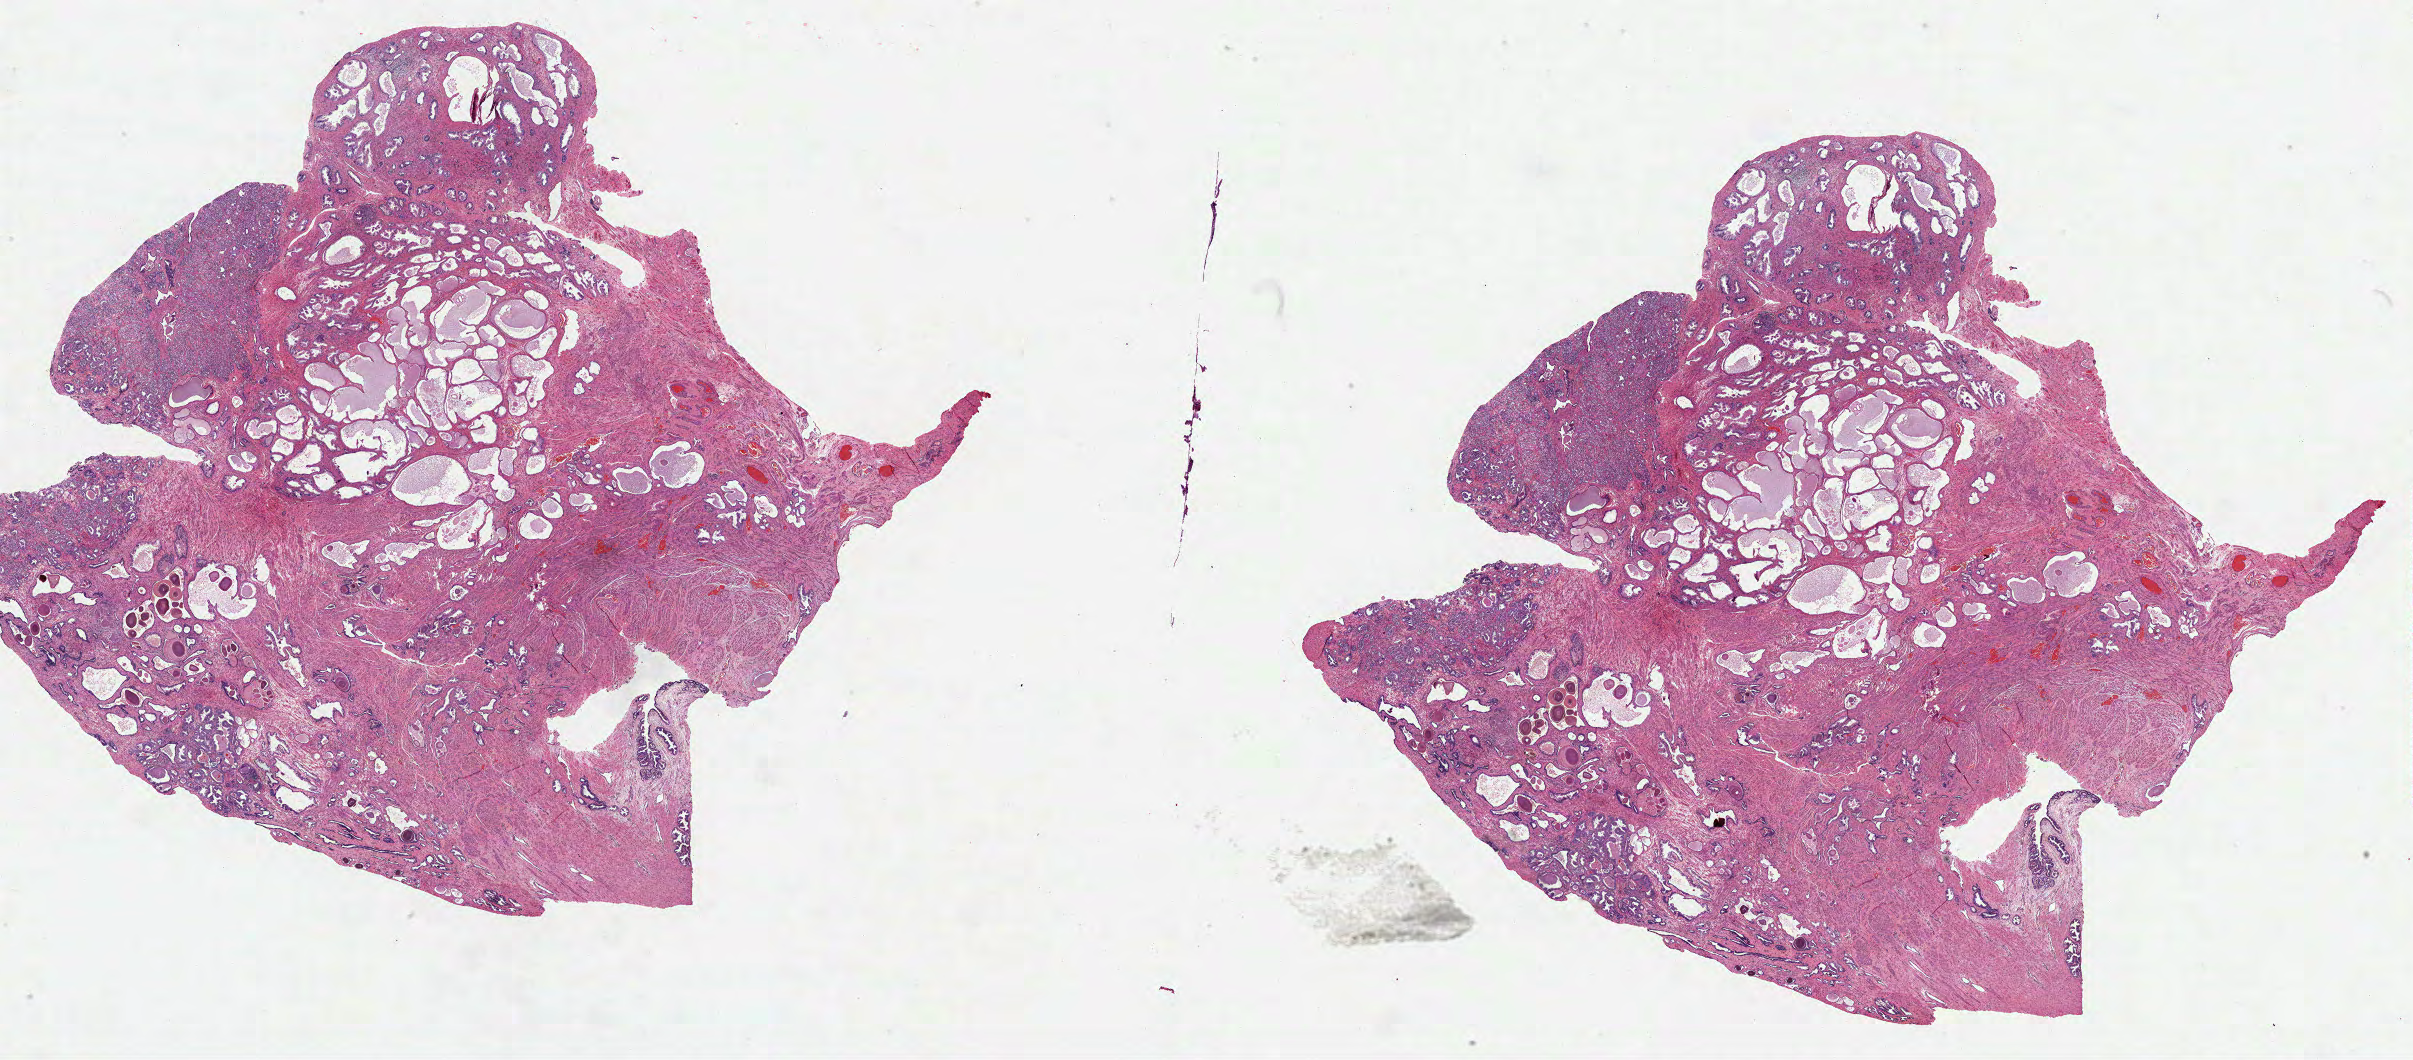
H&E whole-slide image — low-resolution overview of the scanned area, about 38.9 x 17.1 mm (slide scanned at 40x); FFPE section; primary tumour sample from the prostate. Patient: male, age at initial diagnosis 62 years. Gleason score: 7 (3+4).
Diagnosis: Acinar cell carcinoma (prostate gland). Lymph nodes positive (case pathology): 0 of 5 examined.